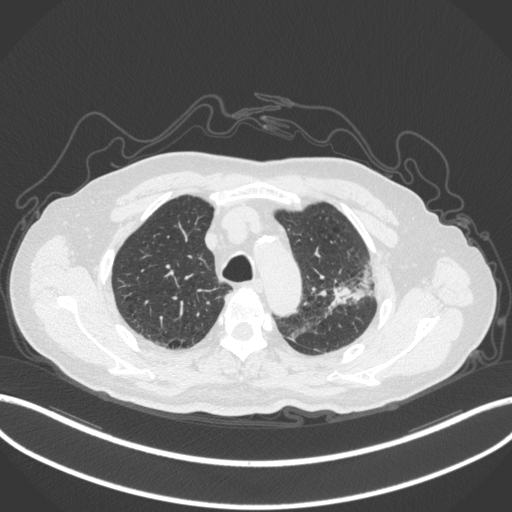
Chest CT, one axial slice. Position 234 of 331 along the scan axis. Reconstruction kernel B31f. 120 kVp. Lung window (W 1500 / L -600 HU). 1 mm slice thickness. 512 × 512 image matrix, field of view 400 × 400 mm. Male patient, age 79 years. From the clinical record (not read from this slice): clinical TNM (as recorded): T2a N1 M1; histopathological grade: G3.
Annotated regions visible in this slice (bounding box drawn by a radiologist):
- lung tumour (recorded histology: adenocarcinoma): bounding box (x1, y1, x2, y2) in pixels: (323, 264, 373, 314)